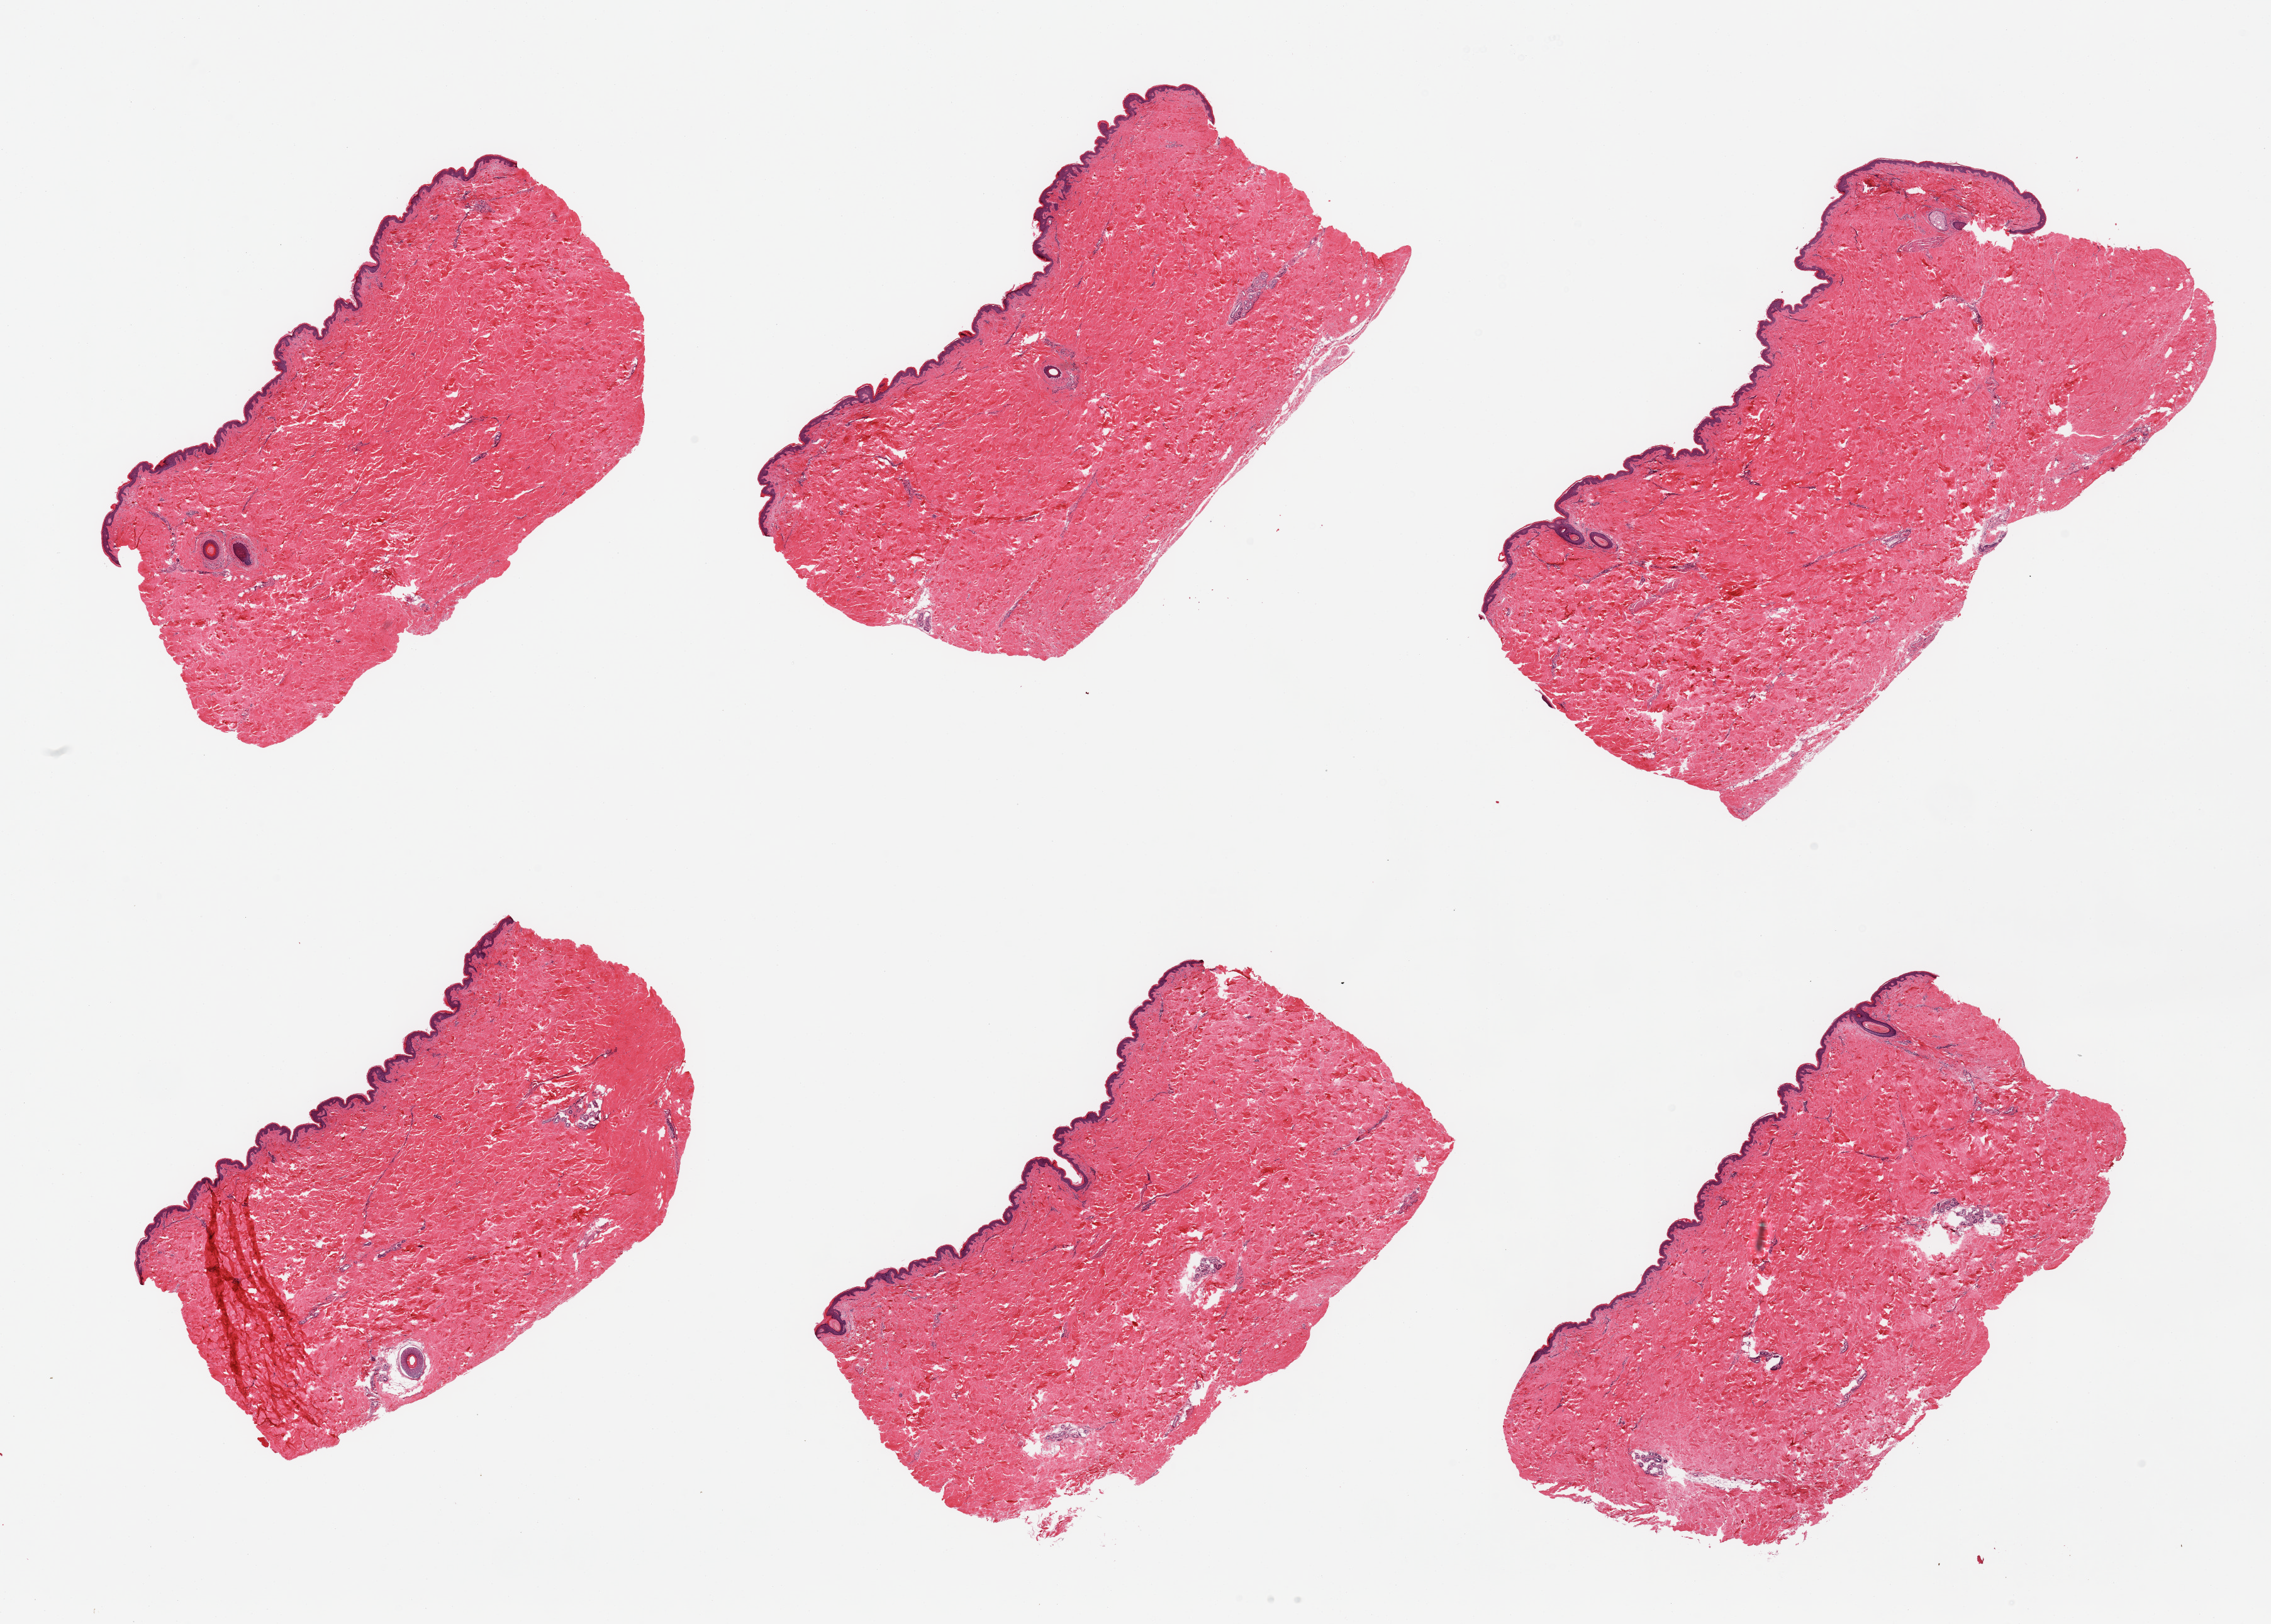
Hematoxylin and eosin (H&E) whole-slide image — shown as a low-resolution overview of the whole scanned area (about 28.5 x 20.4 mm); PAXgene-fixed paraffin-embedded (PFPE) section; sampled site (target tissue): skin of suprapubic region; donor tissue sample. Male donor.
Pathologist's review note for this sample: 6 pieces; well trimmed; <5% dermal fat.